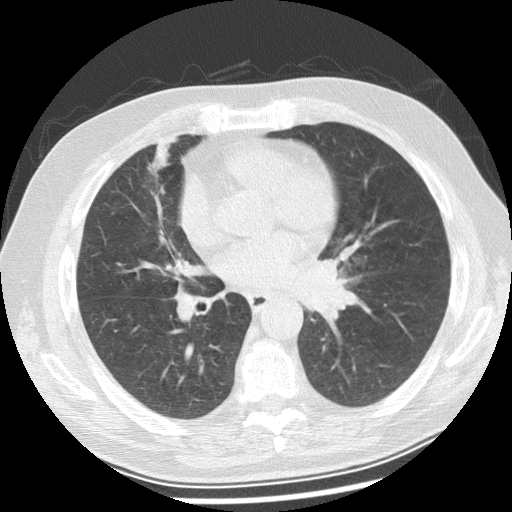
Low-dose screening chest CT, one axial slice; position 126 of 250 along the scan axis; 120 kVp; lung window (W 1500 / L -600 HU); 2.5 mm slice thickness; 512 × 512 image matrix, field of view 360 × 360 mm.
Outlined on this slice (expert manual segmentation):
- lesion 1 (tumor, left main bronchus): box from (x=293, y=258) to (x=358, y=316) px